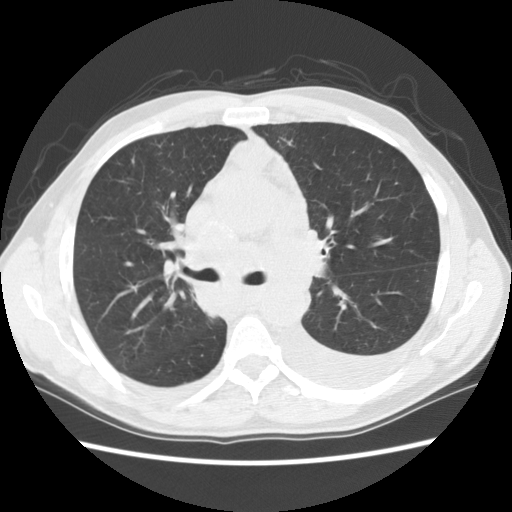
Low-dose screening chest CT, axial slice. Baseline screening round. Lung window (W 1500 / L -600 HU). 2.5 mm slice thickness. Standard (soft-tissue) reconstruction kernel (STANDARD). Slice 43 of 135 in the series. Male, age 60 years at enrolment. Current smoker at enrolment.
- Expert reader's lesion annotation, bounding box (x1, y1, x2, y2) in pixels: (178, 236, 292, 326).
- No non-calcified nodule or mass ≥4 mm was recorded by the screening reader at this exam.
- Lung cancer was diagnosed 12 days after this screen: squamous cell carcinoma, NOS, carina, poorly differentiated (G3), stage IV (AJCC 6th edition).